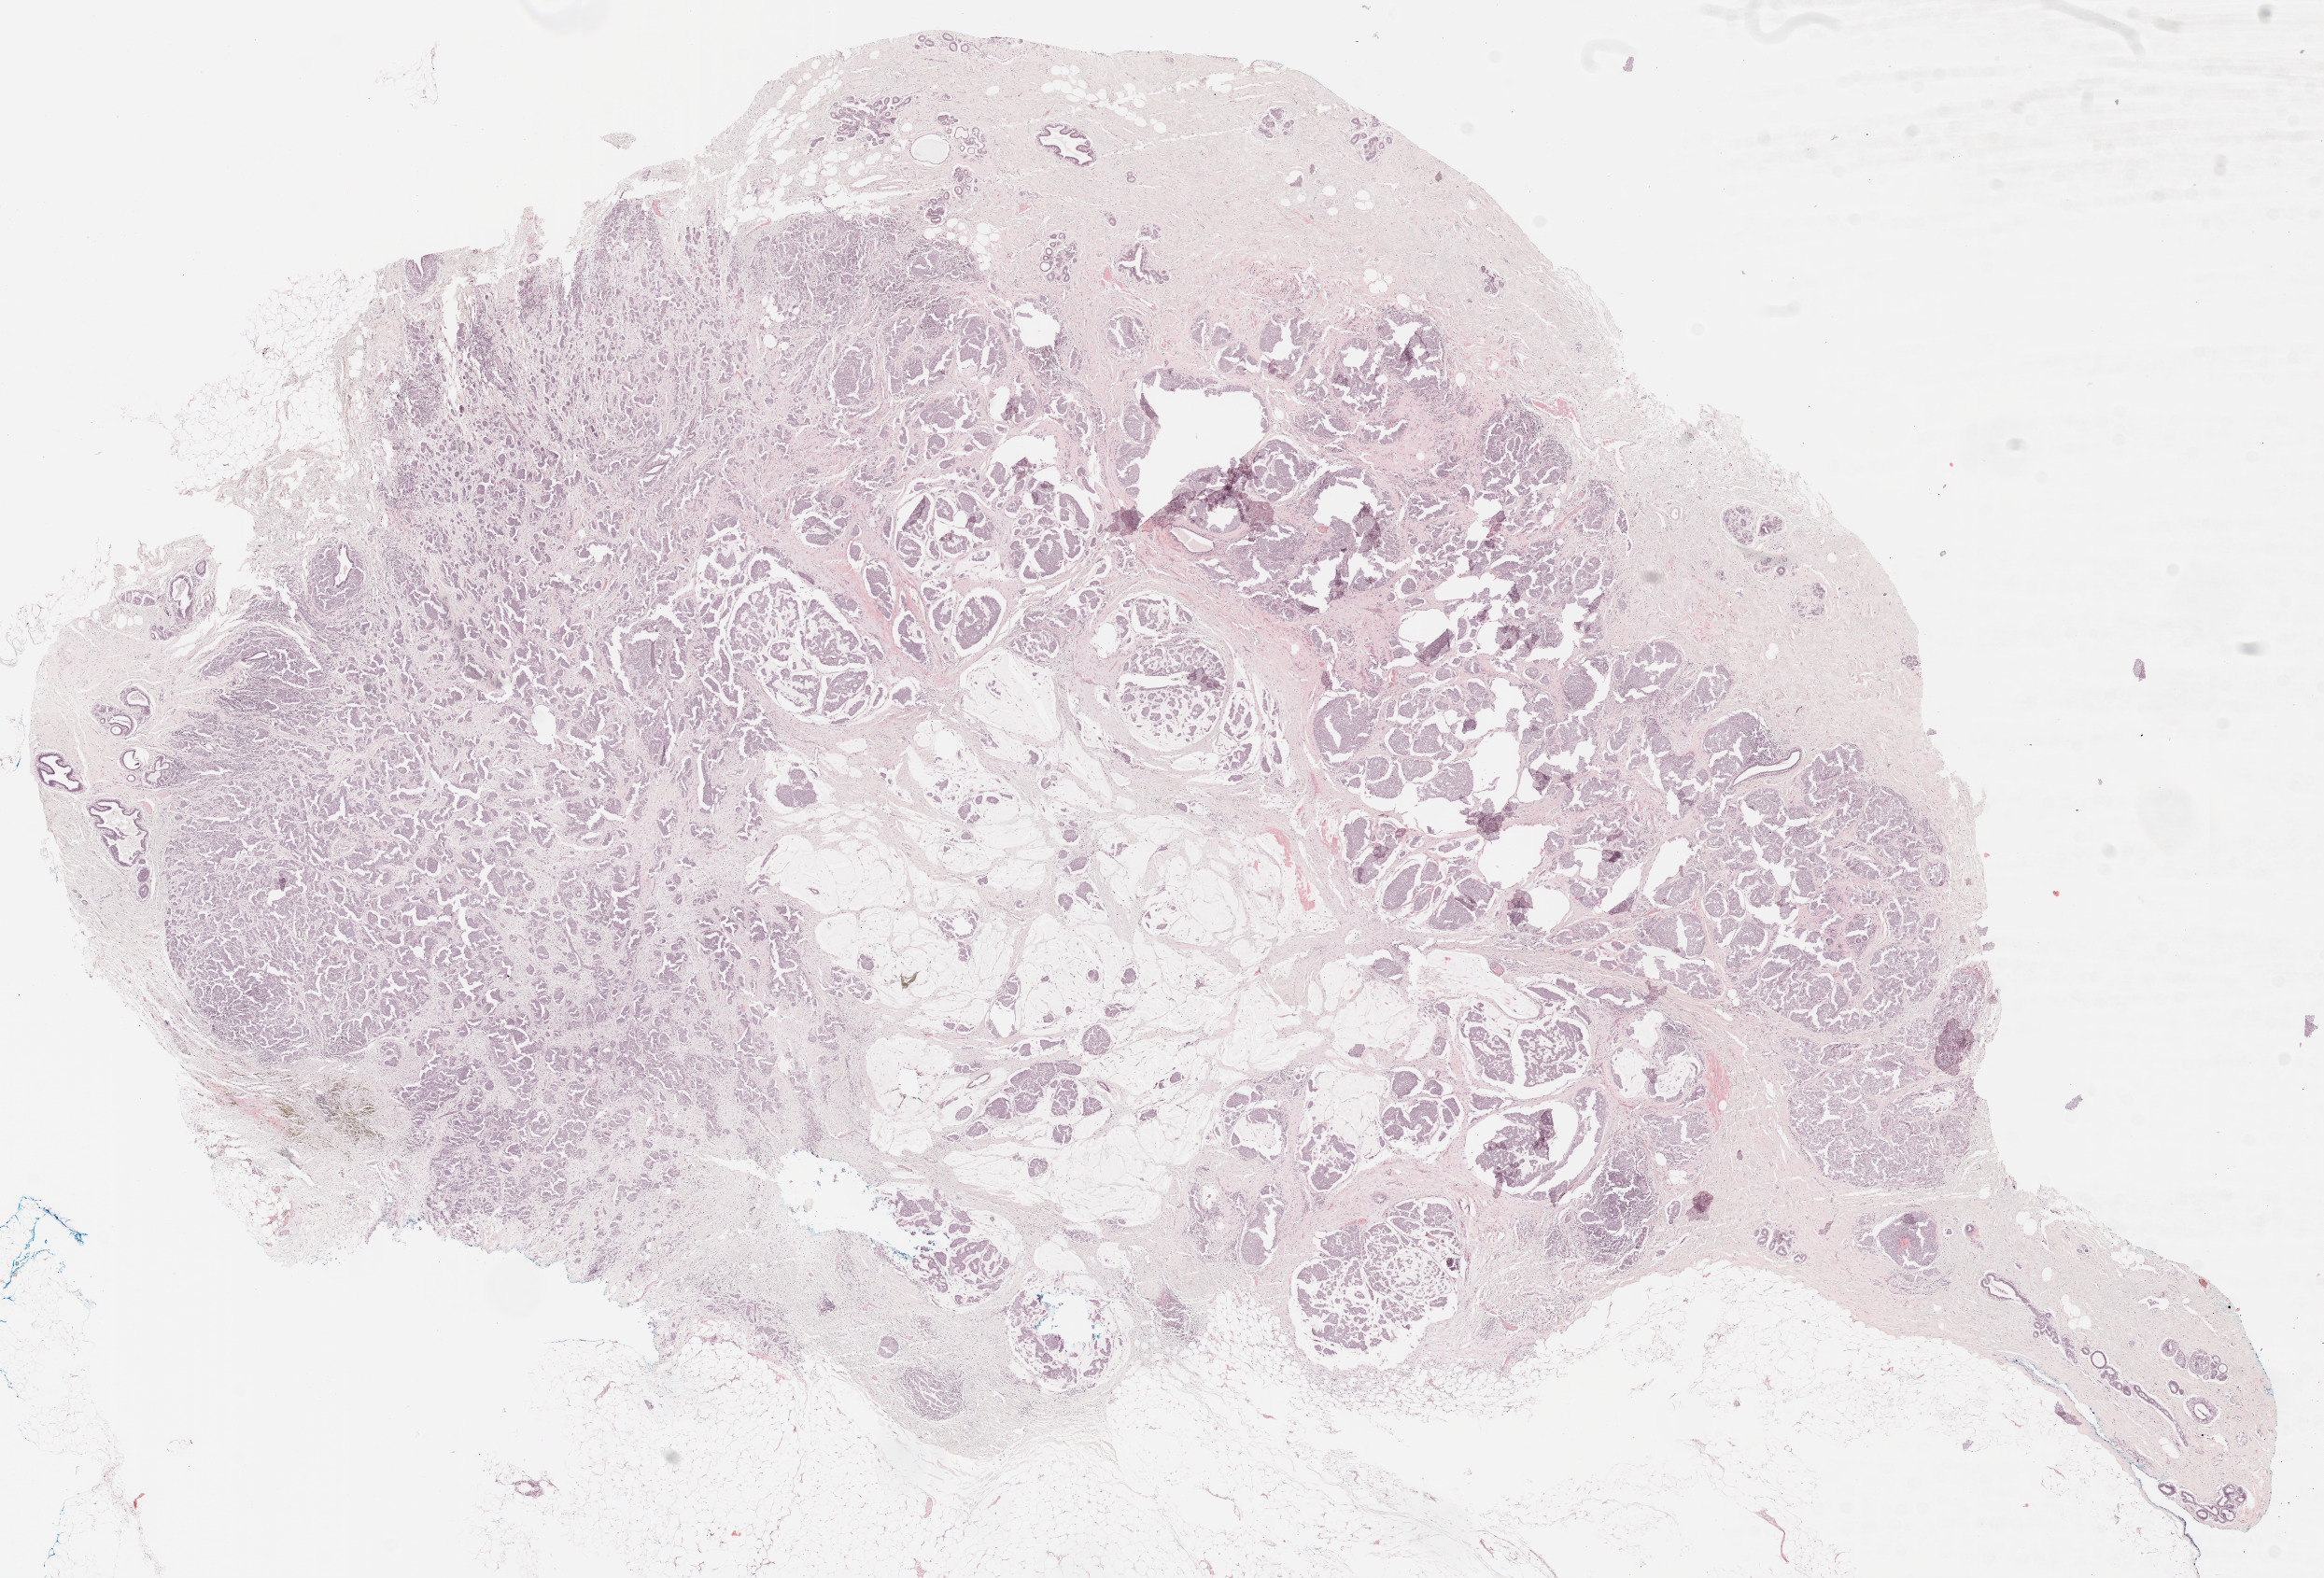
Hematoxylin and eosin (H&E) stained whole-slide image, low-resolution overview of the scanned area, about 19.9 x 13.5 mm; formalin-fixed paraffin-embedded (FFPE) diagnostic section; primary tumour sample from the breast. Female, age 49 years at initial diagnosis.
Pathologic diagnosis: Infiltrating duct mixed with other types of carcinoma. Laterality: right. Lymph nodes positive (case pathology): 4 of 19 examined. AJCC pathologic stage: IIIA.